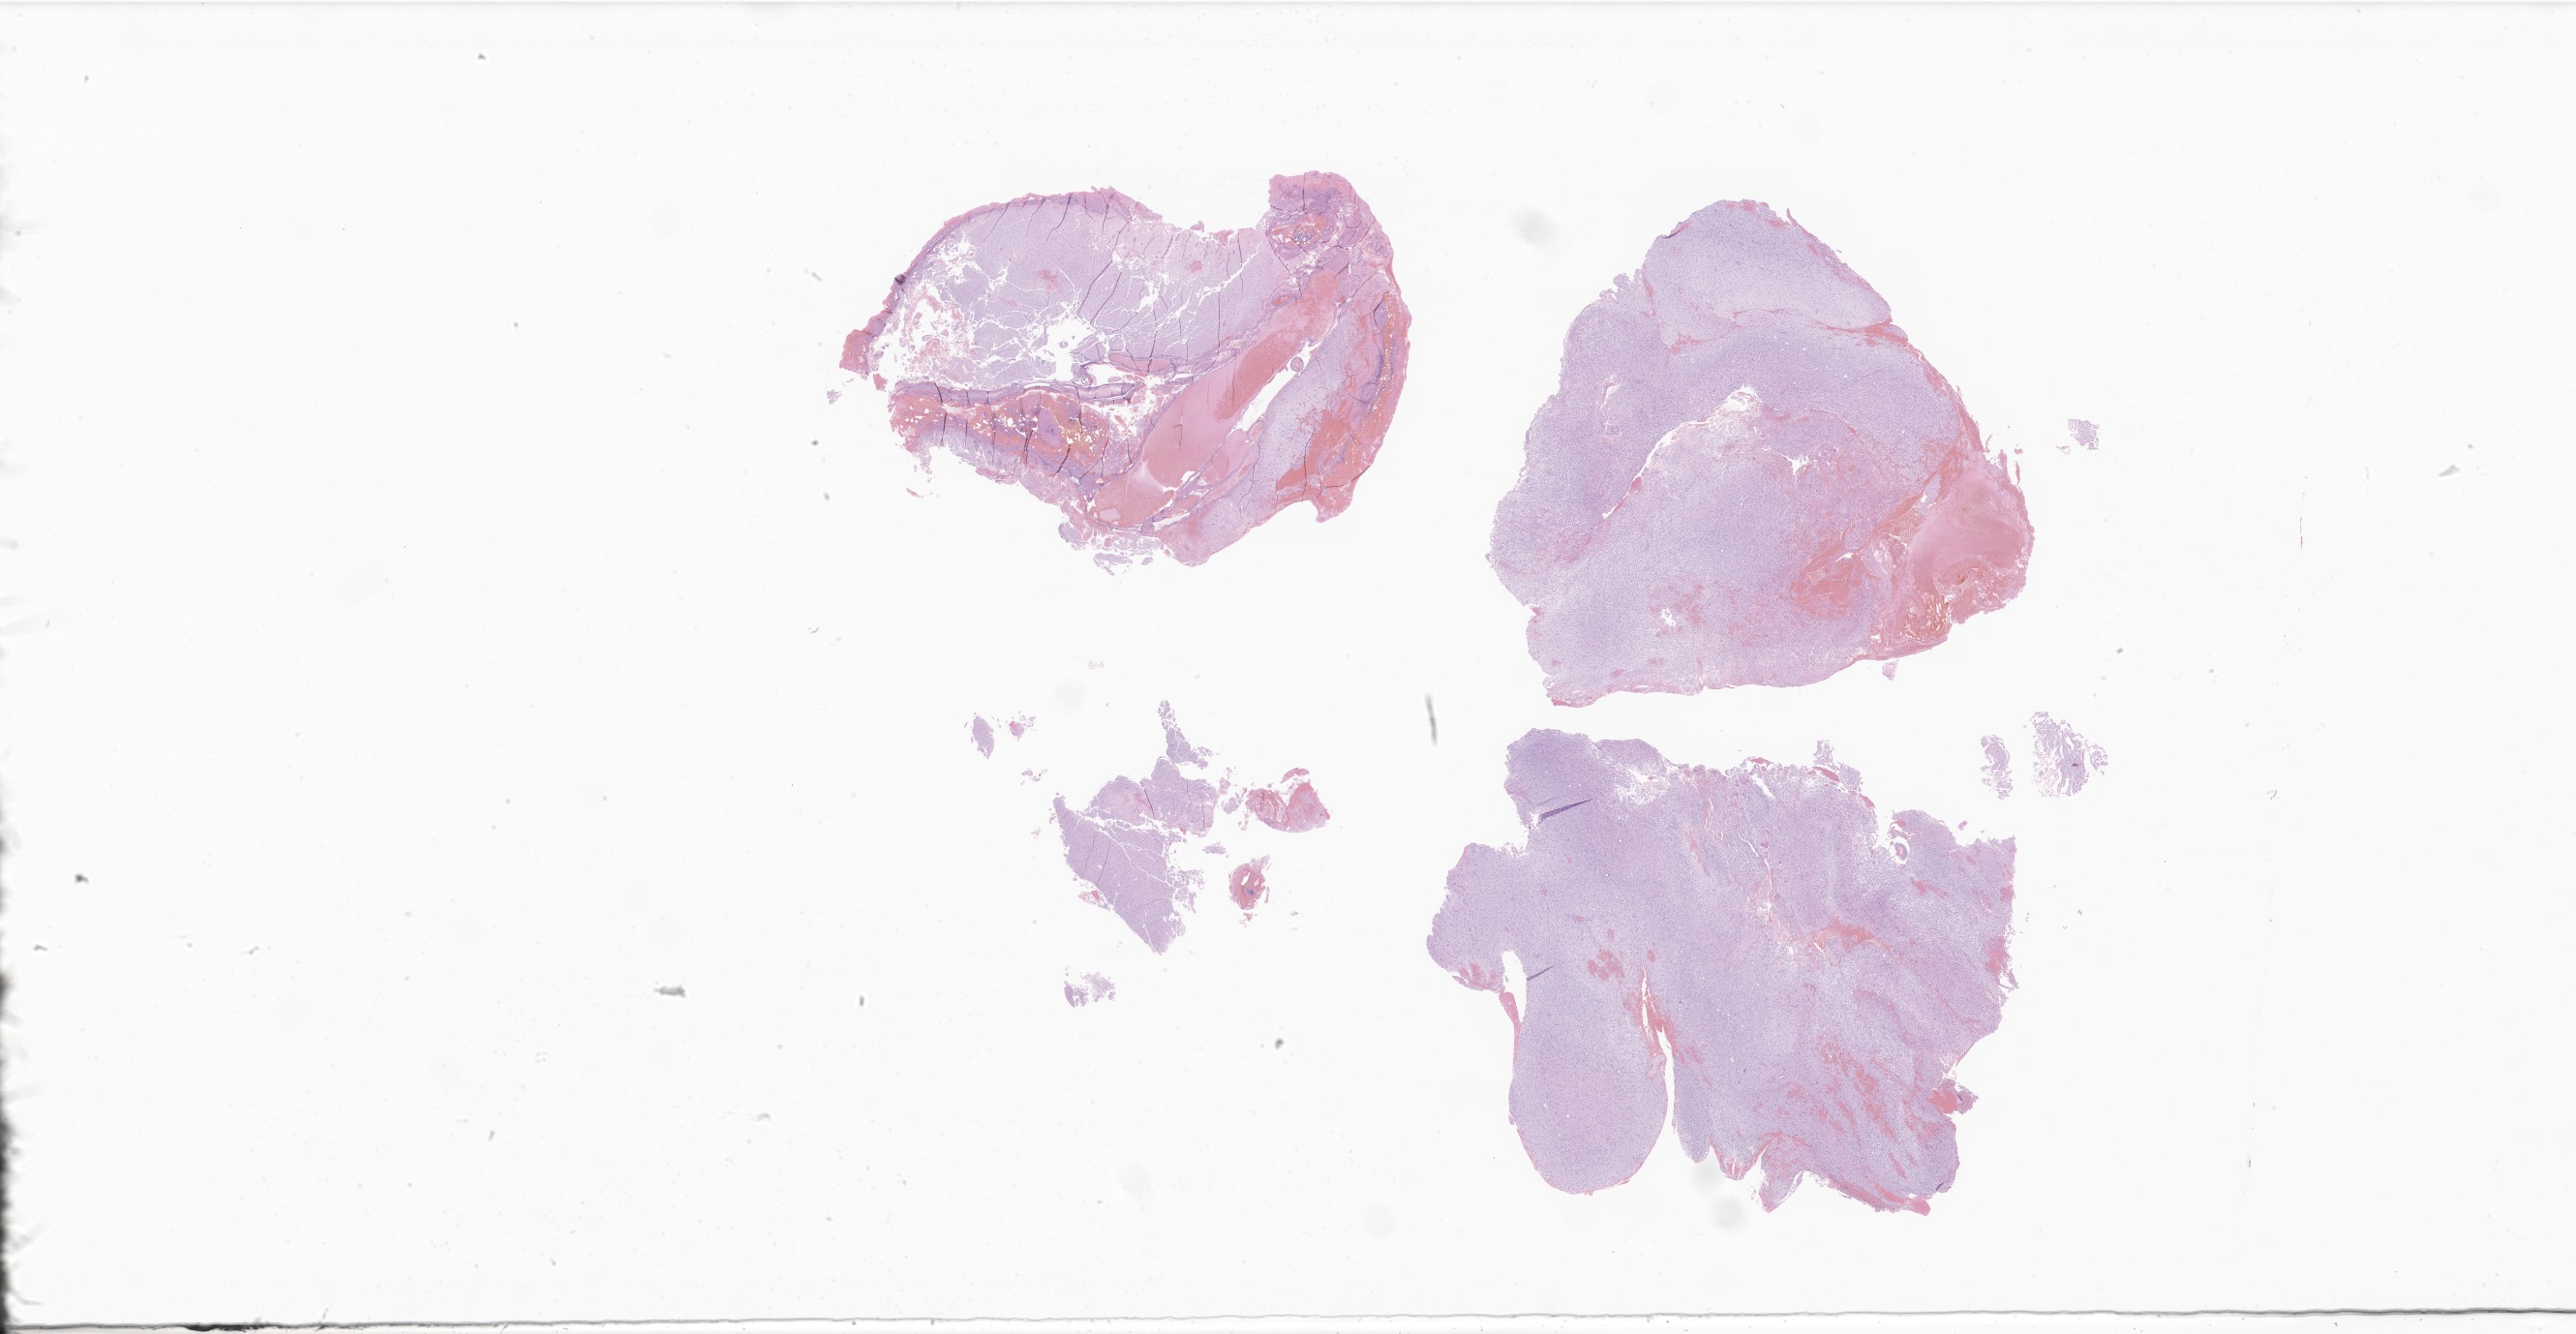
Digitized haematoxylin and eosin-stained section of tumor tissue from the brain — whole scanned area (about 44.9 x 23.2 mm) shown as a low-resolution overview; formalin-fixed, paraffin-embedded (FFPE) tissue. Patient female; age 206 months (17 years 2 months).
- recorded diagnosis: Glioblastoma, NOS